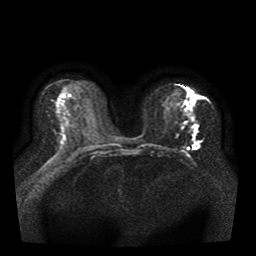
Breast MRI, one axial slice. Slice 18 of 41 in the series (ordered by position). Diffusion-weighted series; image 2 of 4 stored at this slice position (different b-values; order by instance number). 1.5 T. 5 mm slice thickness. 256 × 256 image matrix, field of view 330 × 330 mm. Female patient.
Outlined on this slice (manually delineated by an expert):
- tumour on diffusion-weighted imaging: box from (x=193, y=95) to (x=199, y=145) px